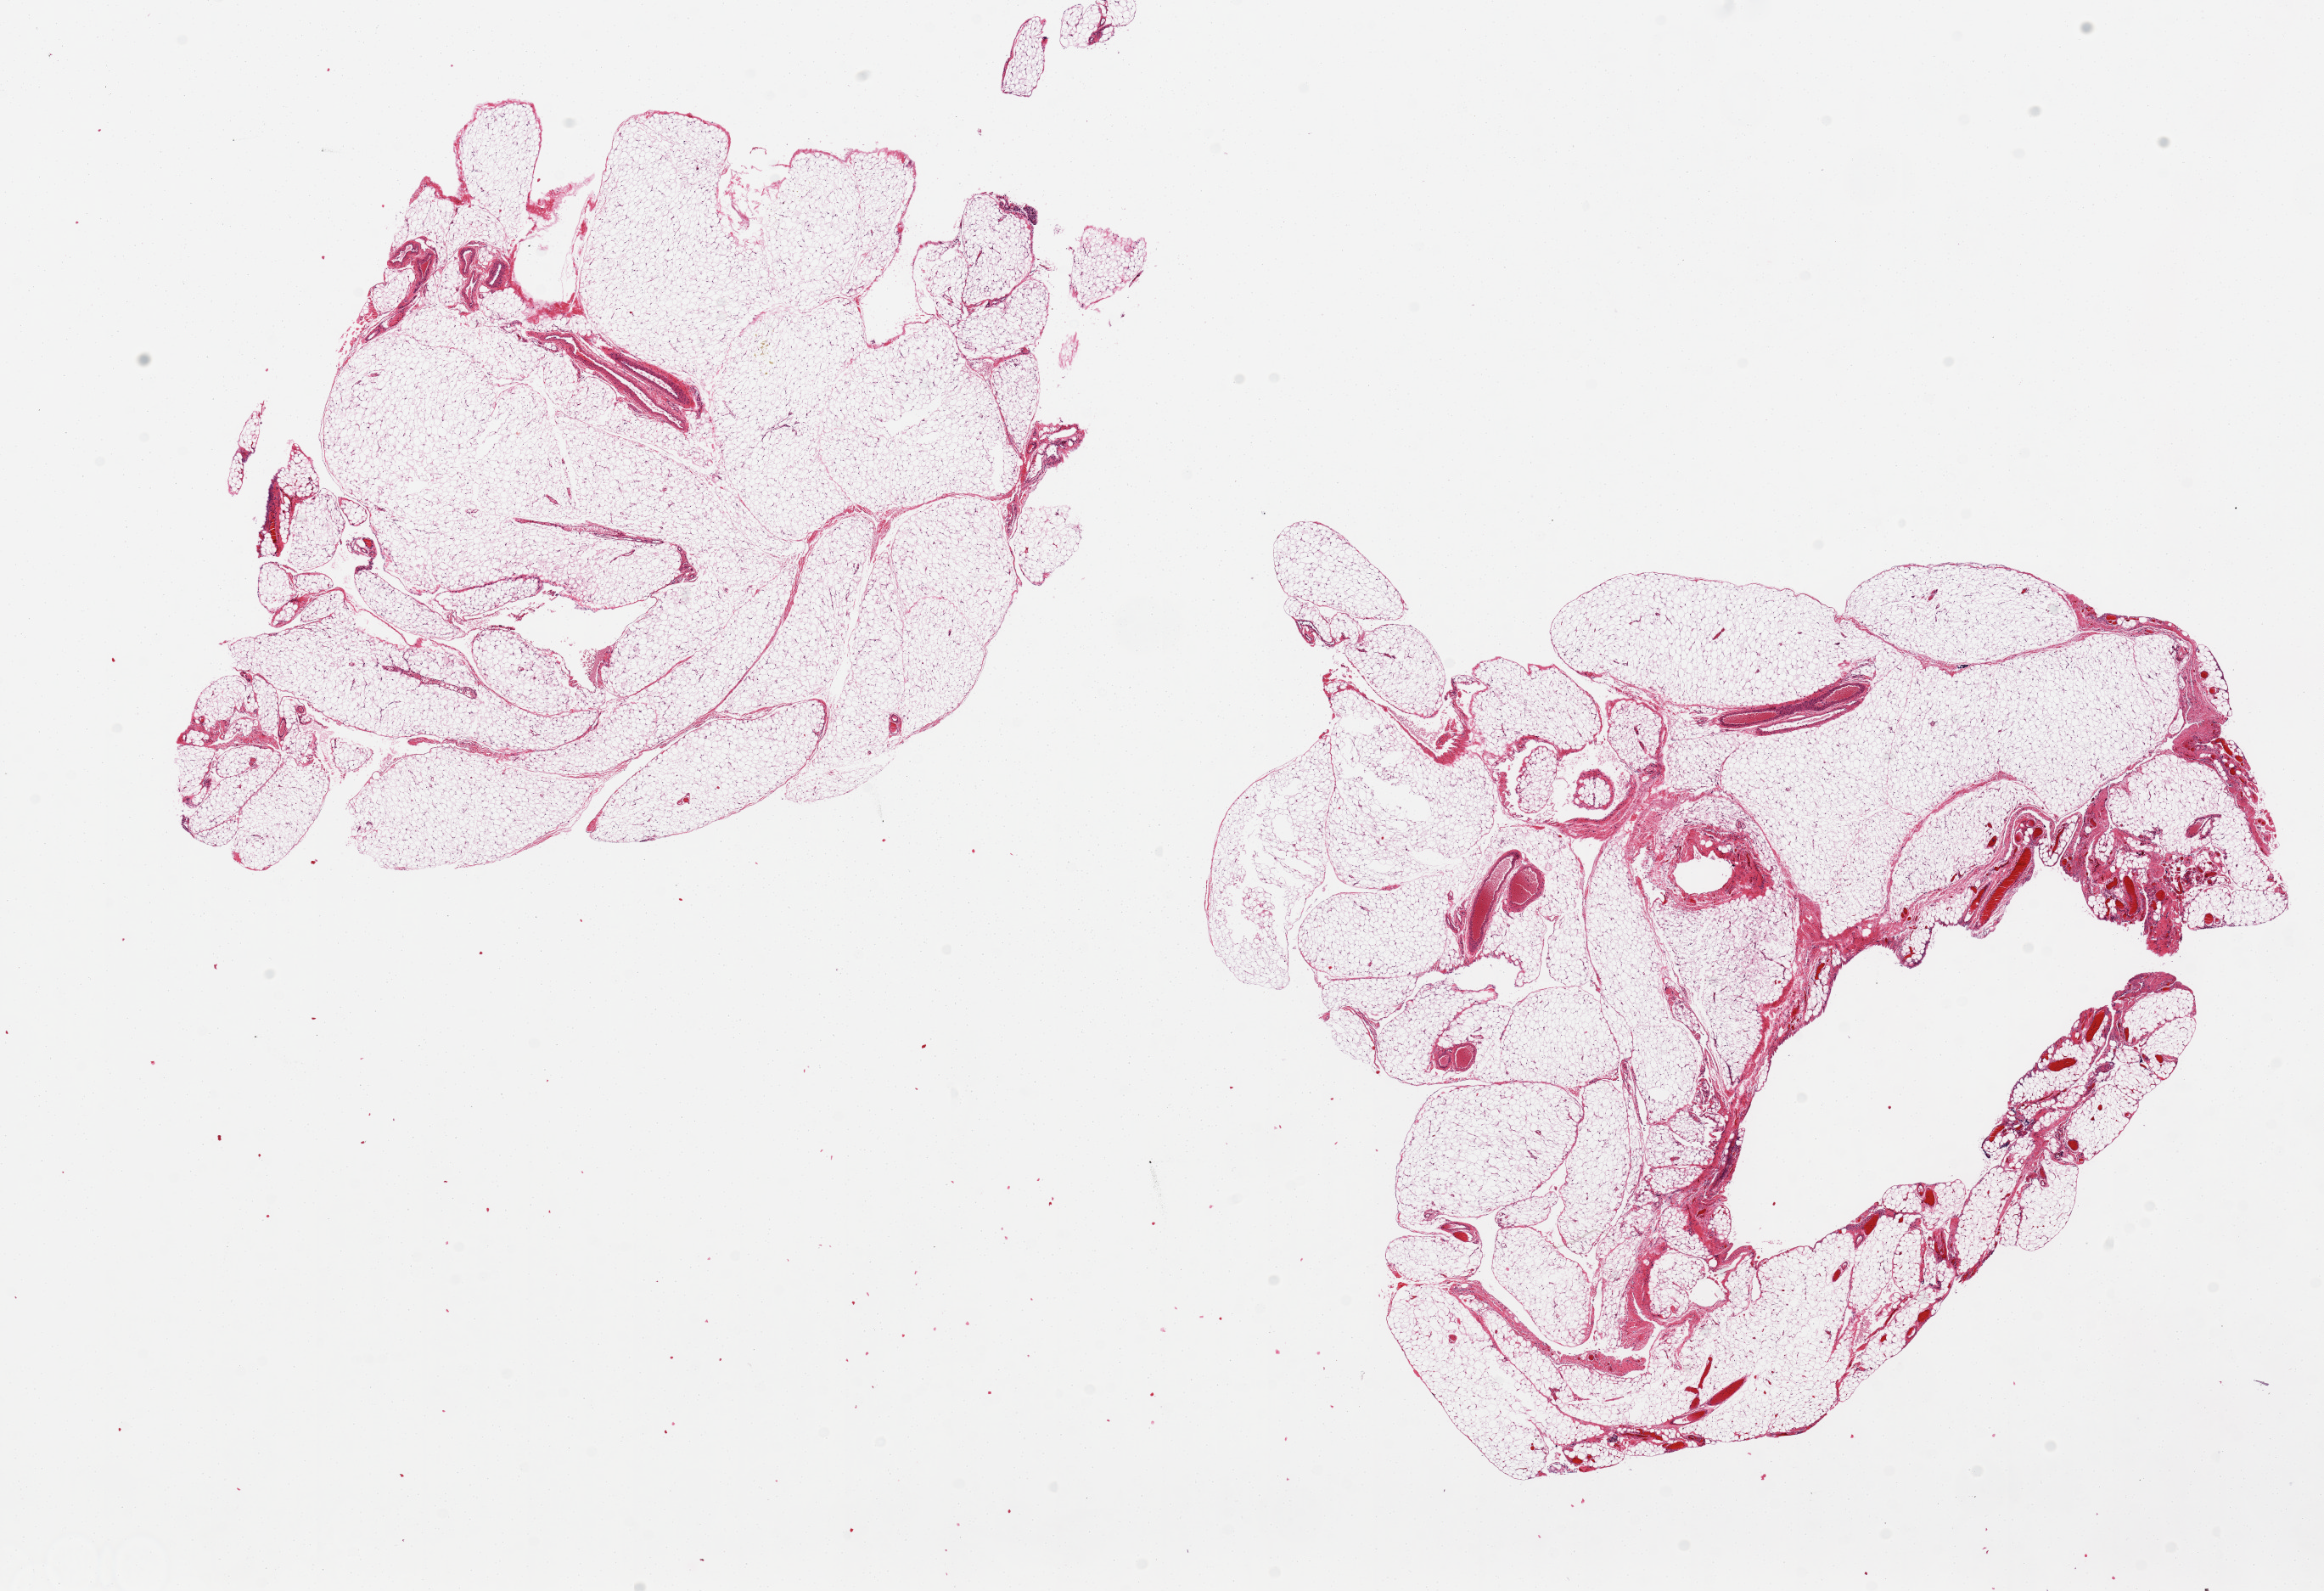
H&E whole-slide image, a low-resolution overview of the entire scanned area, about 21.7 x 14.8 mm (slide scanned at 20x). PAXgene-fixed, paraffin-embedded tissue. Section of omentum (target tissue). Donor tissue sample. Donor: female.
Review note (as recorded): 2 pieces, fat with few larger vessels.